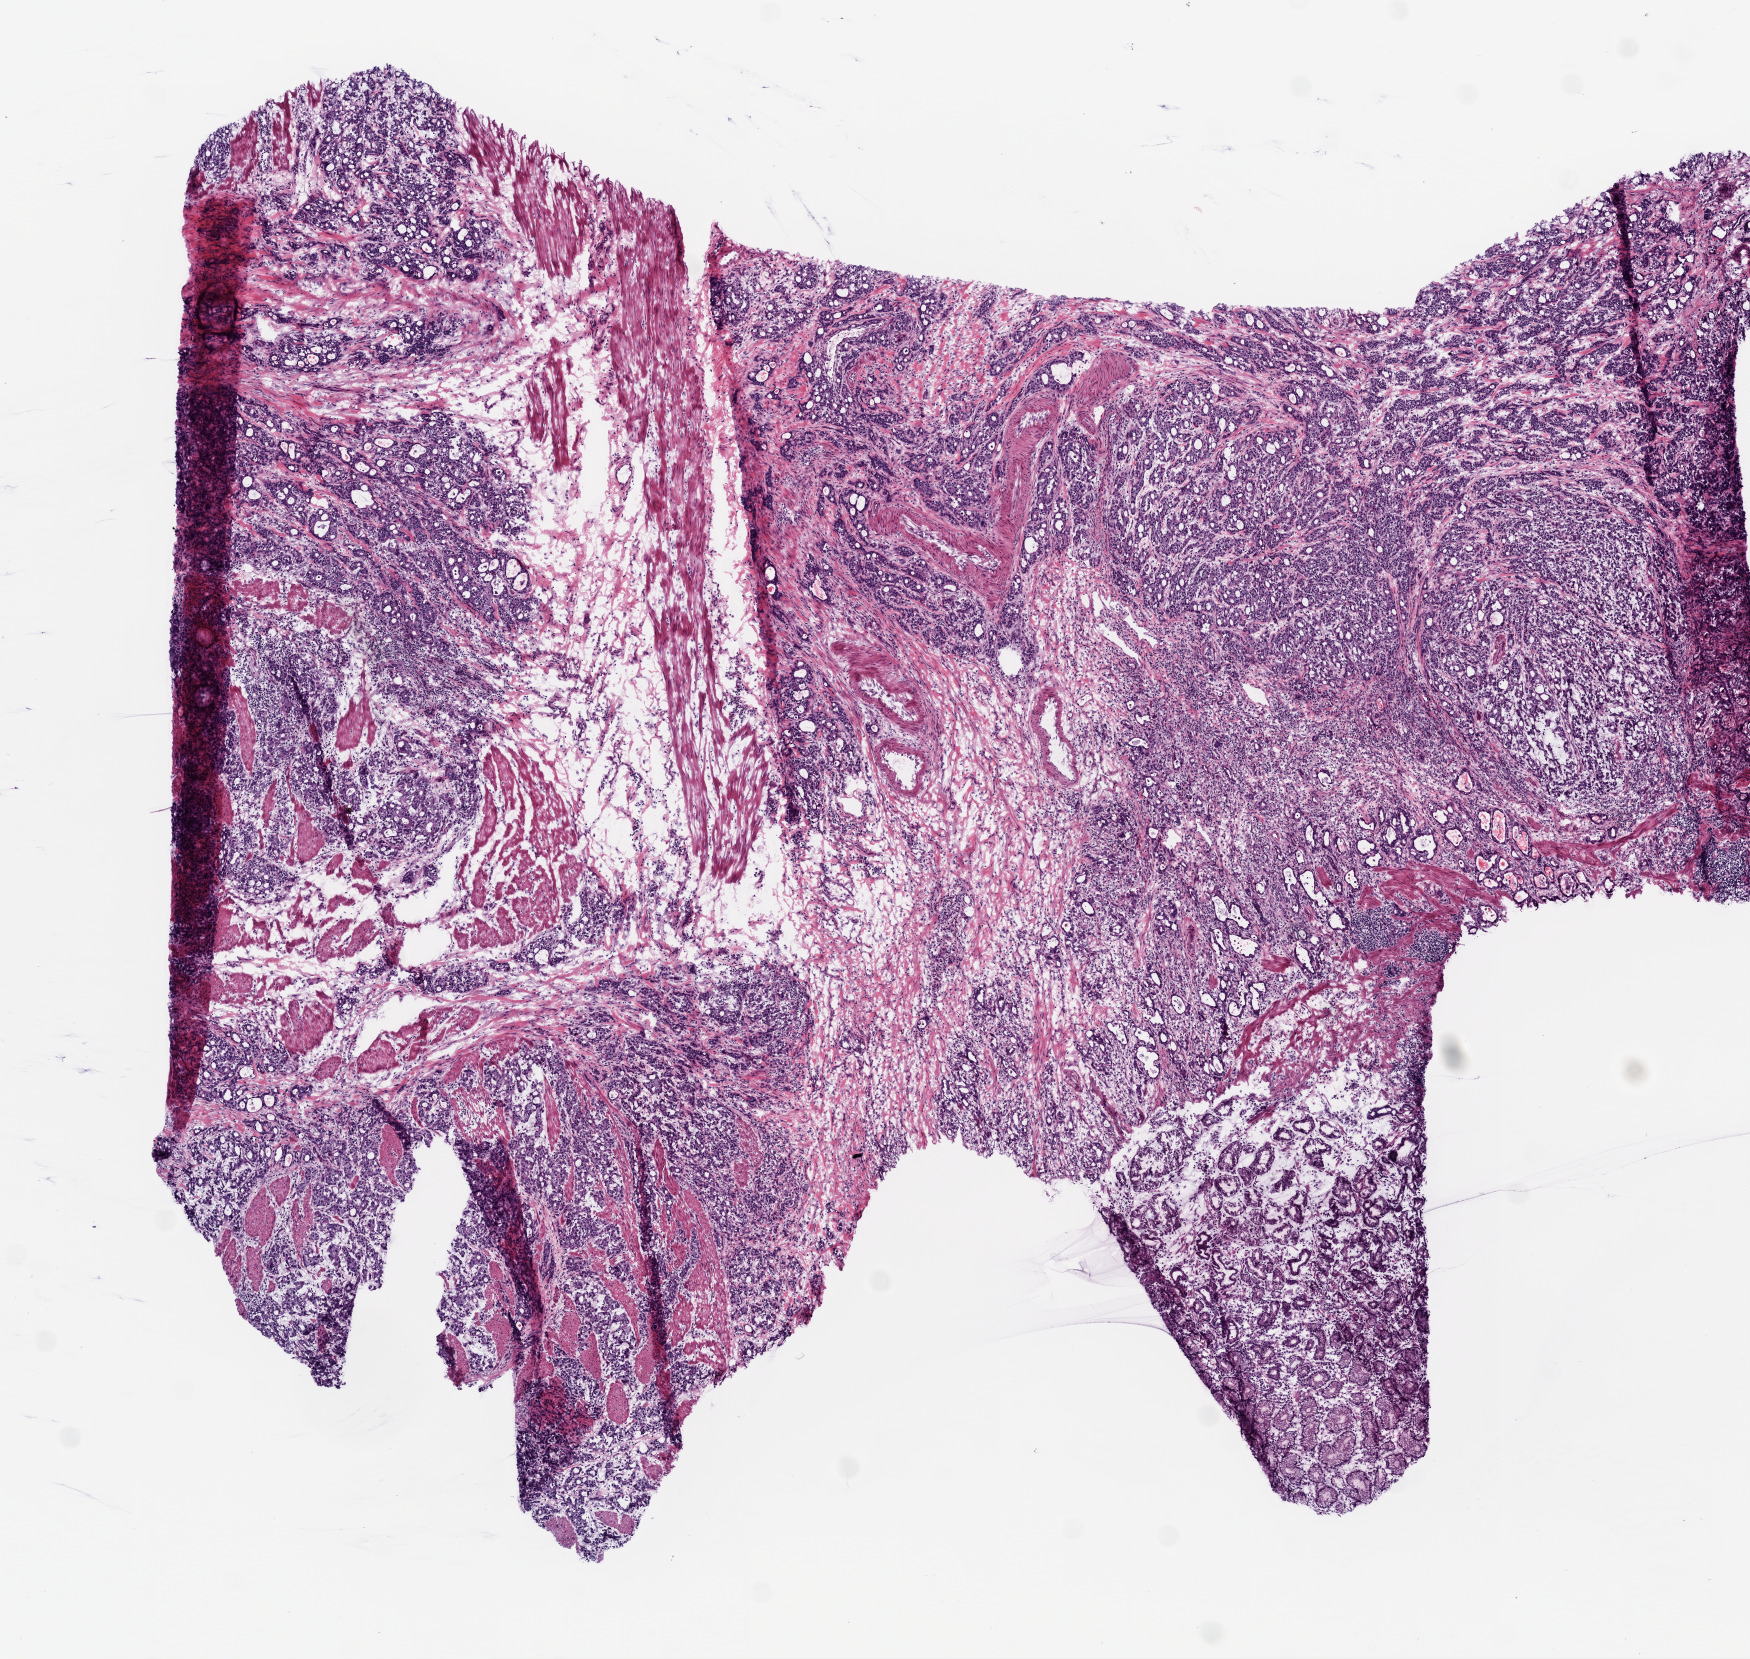
Hematoxylin and eosin (H&E) stained whole-slide image — whole scanned area (about 7.0 x 6.7 mm, from a 20x scan) shown as a low-resolution overview. Frozen section from the bottom of the tissue portion. Stomach, primary tumour sample. Male patient; age at initial diagnosis 49 years. Histologic grade: G3 (poorly differentiated). Composition of this section per pathologist review: tumour cells 83%, tumour nuclei 75%, normal cells 5%, stromal cells 10%, necrosis 2%.
TNM: T4 N1 M0. Histologic diagnosis: Adenocarcinoma with mixed subtypes (gastric antrum). AJCC pathologic stage: IV (6th edition). Lymph nodes positive (case pathology): 5 of 29 examined.